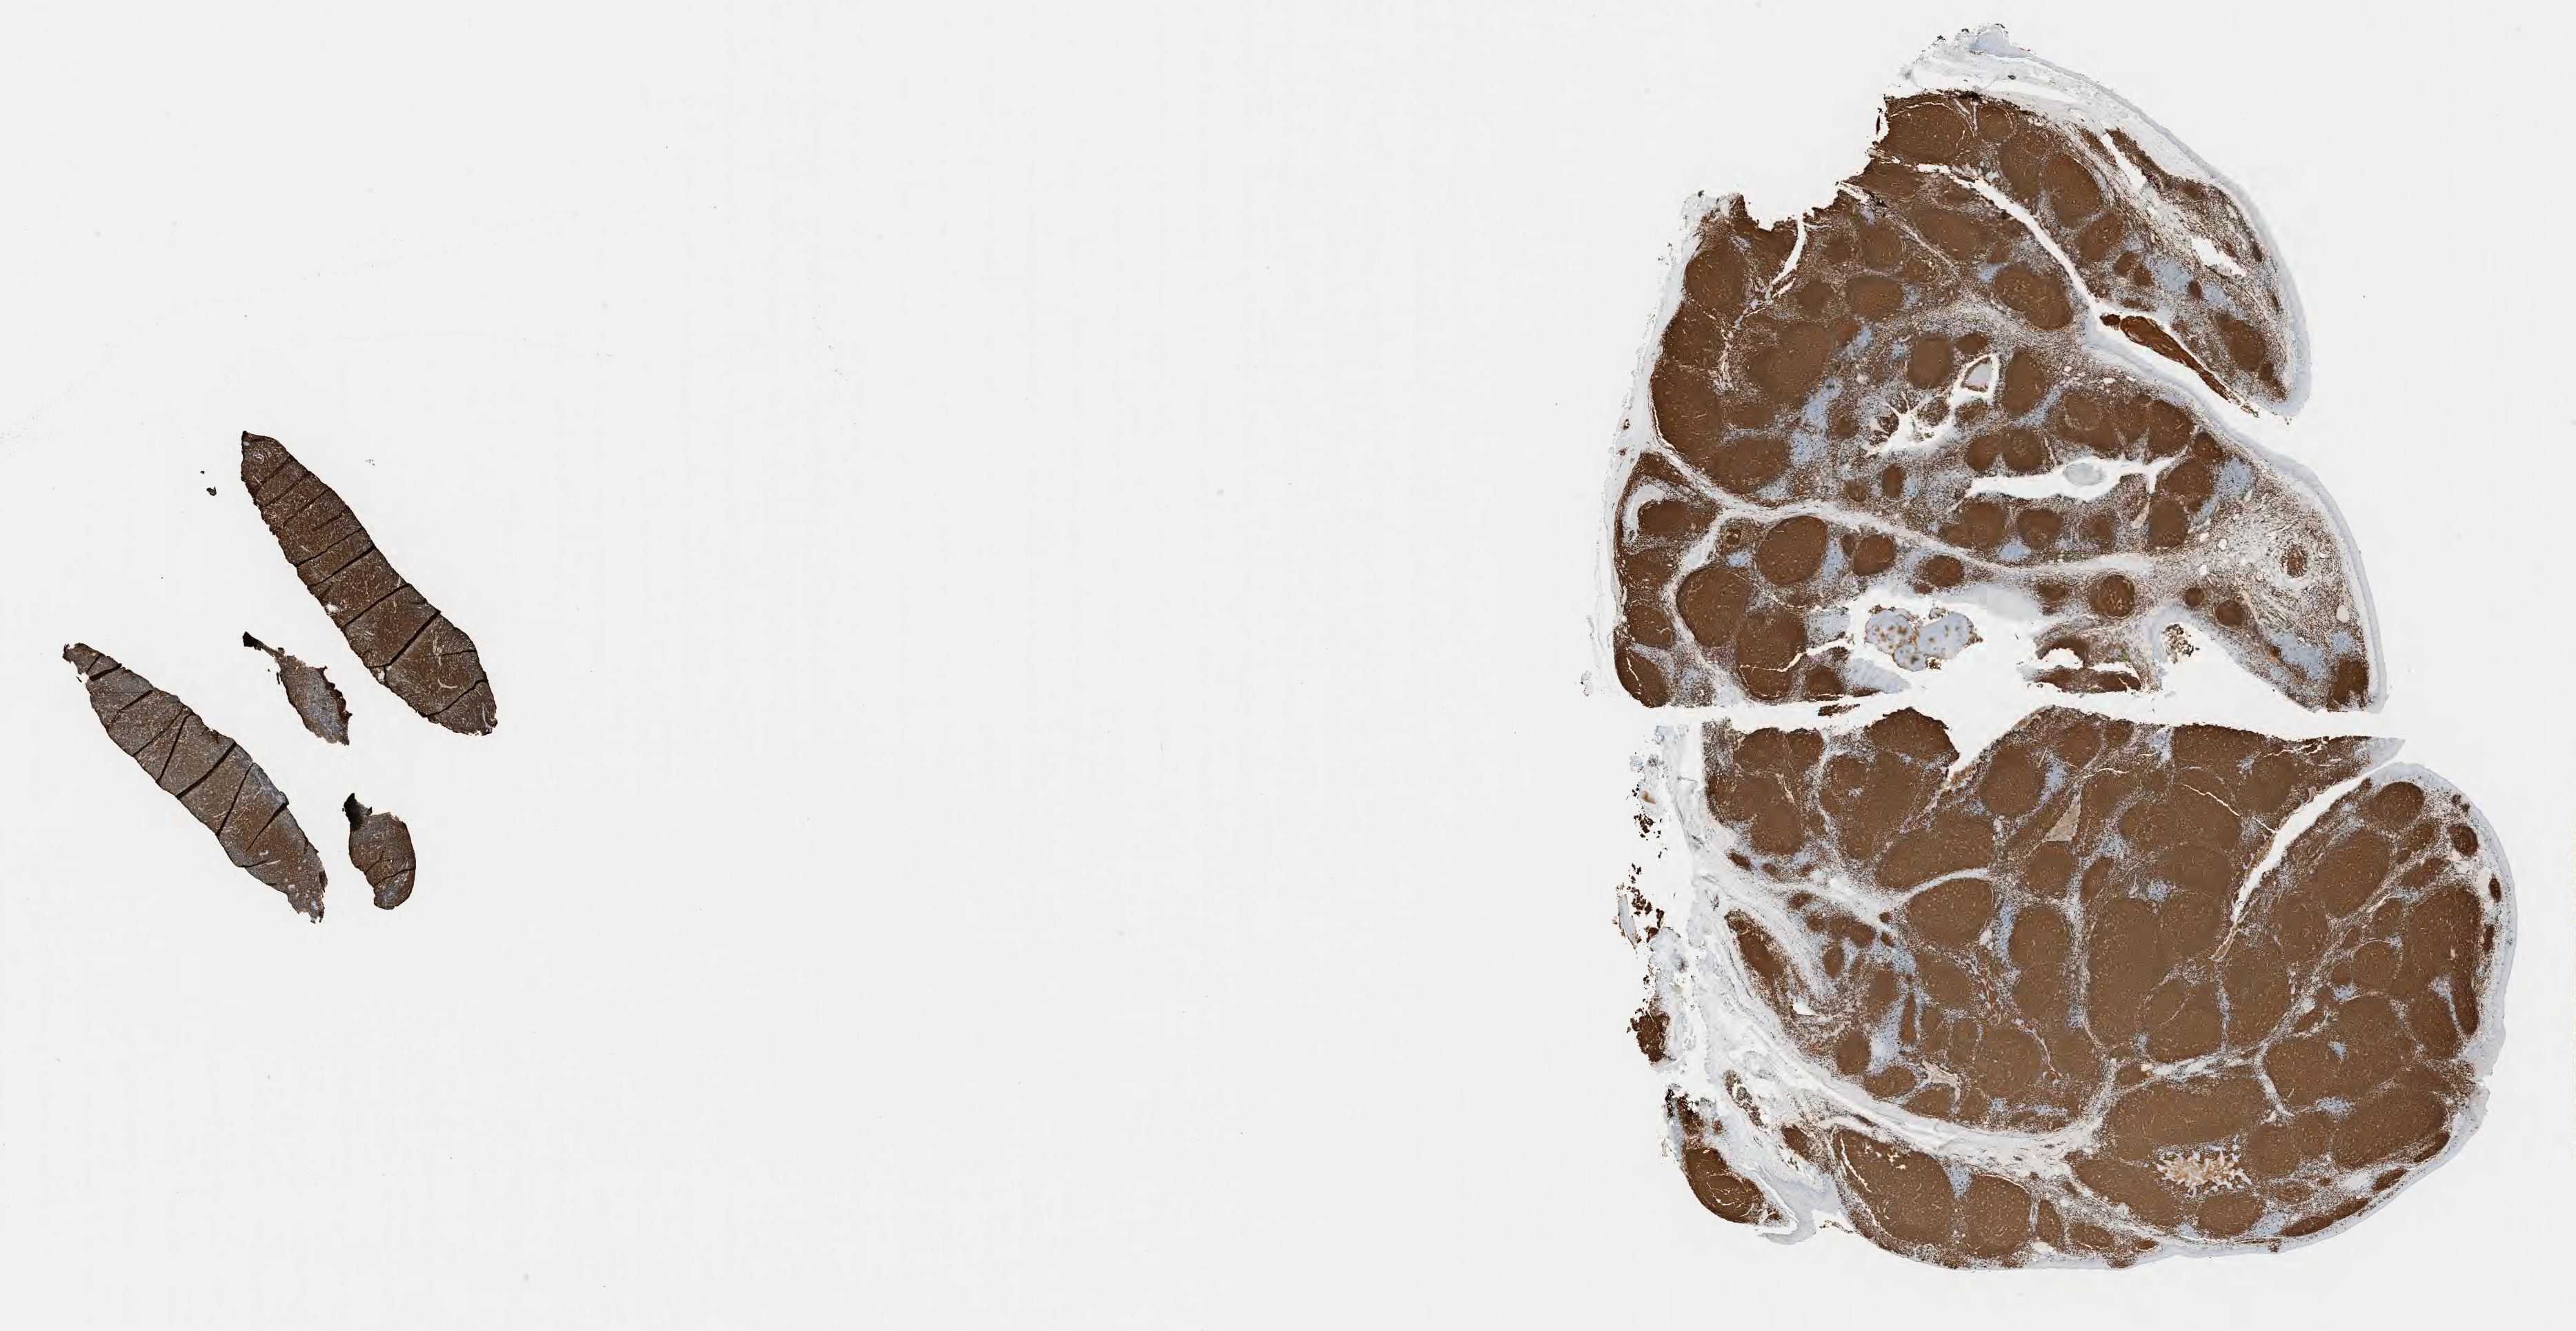
Whole-slide image, immunohistochemical stain for CD20, shown as a low-resolution overview of the whole scanned area (about 30.2 x 15.6 mm), specimen: tumor tissue. Female patient, aged 46.
Diagnosis: Burkitt lymphoma, NOS.